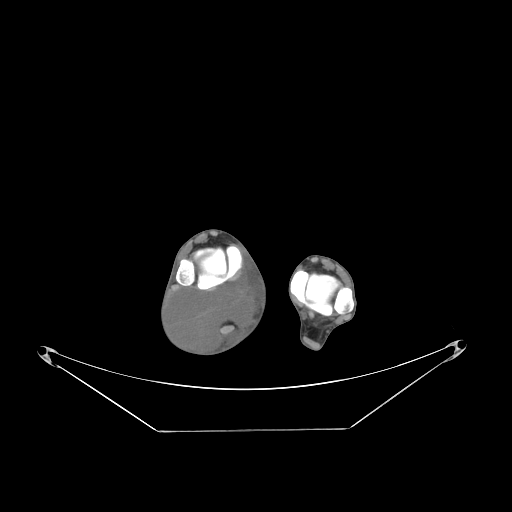
CT of an extremity soft-tissue mass (from a PET/CT study), one axial slice. Position 47 of 267 along the scan axis. Reconstruction kernel STANDARD. 140 kVp. Soft-tissue window (W 400 / L 40 HU). 512 × 512 image matrix, field of view 500 × 500 mm. Male patient. From the clinical record (not read from this slice): histological type: liposarcoma - round cell; grade: high; site of the primary tumour: right calf.
Outlined on this slice (expert contour drawn on MRI and transferred to this co-registered scan by the dataset authors):
- gross tumour volume (mass): box from (x=169, y=276) to (x=257, y=352) px